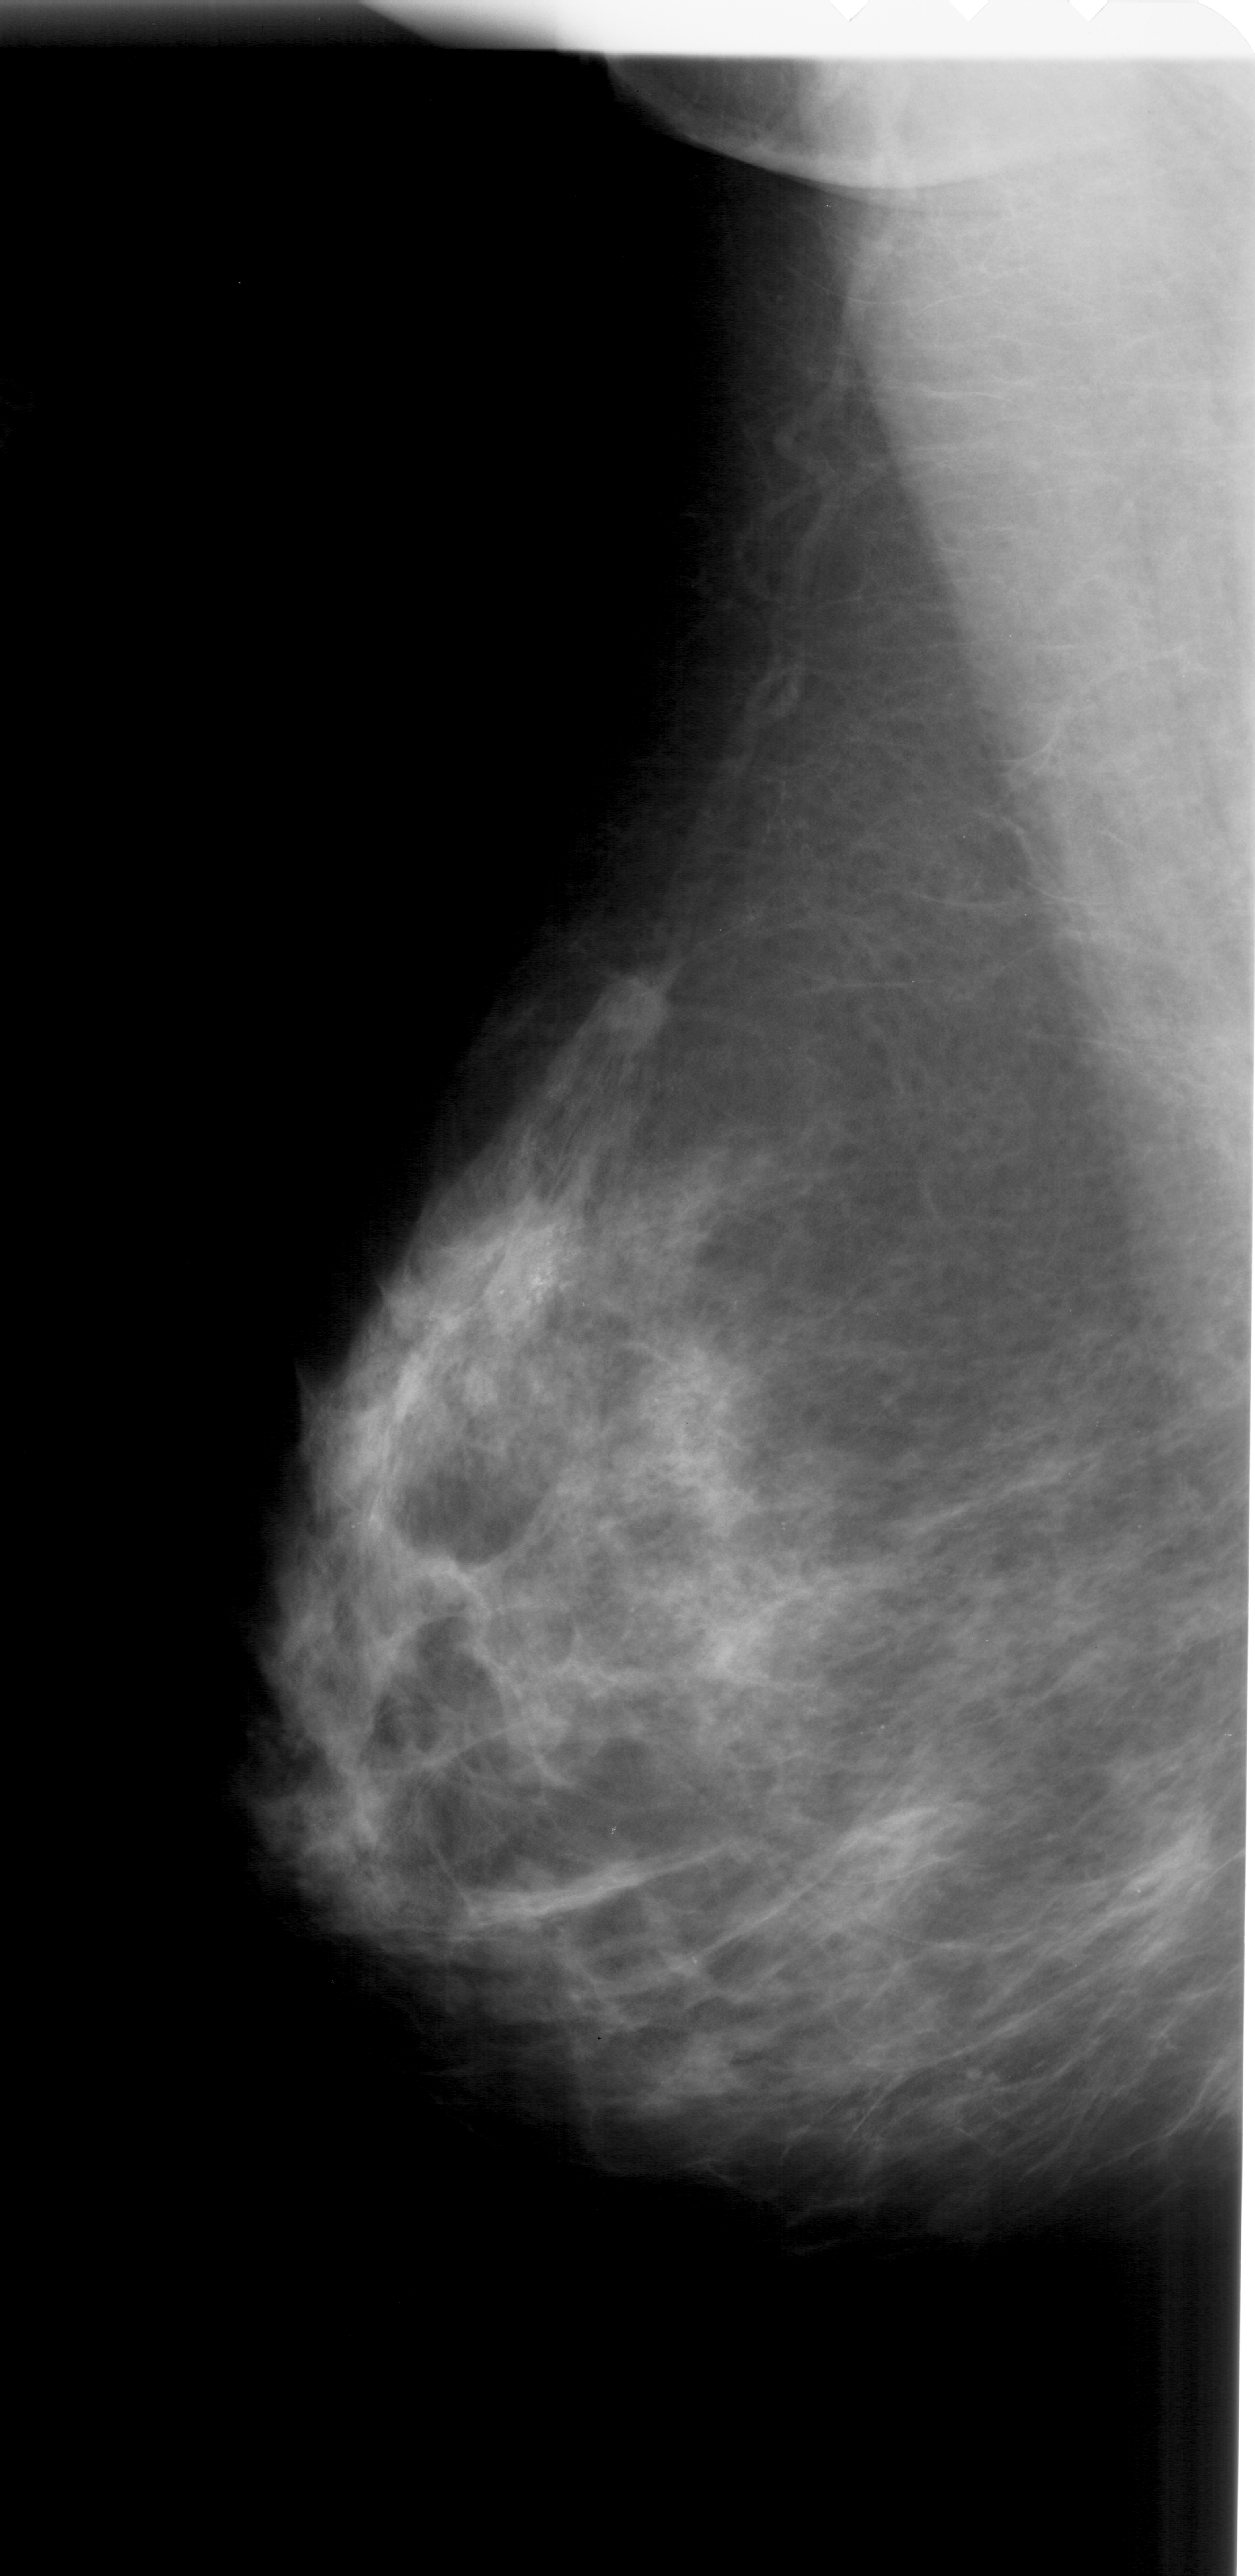
Digitized screen-film mammogram; left breast; MLO view; 1255 × 2576 image matrix.
Marked abnormalities (boxes around the expert regions of interest):
- calcifications, morphology pleomorphic, distribution clustered; BI-RADS assessment category 4; pathology (as recorded): malignant: box from (x=480, y=1201) to (x=597, y=1347) px